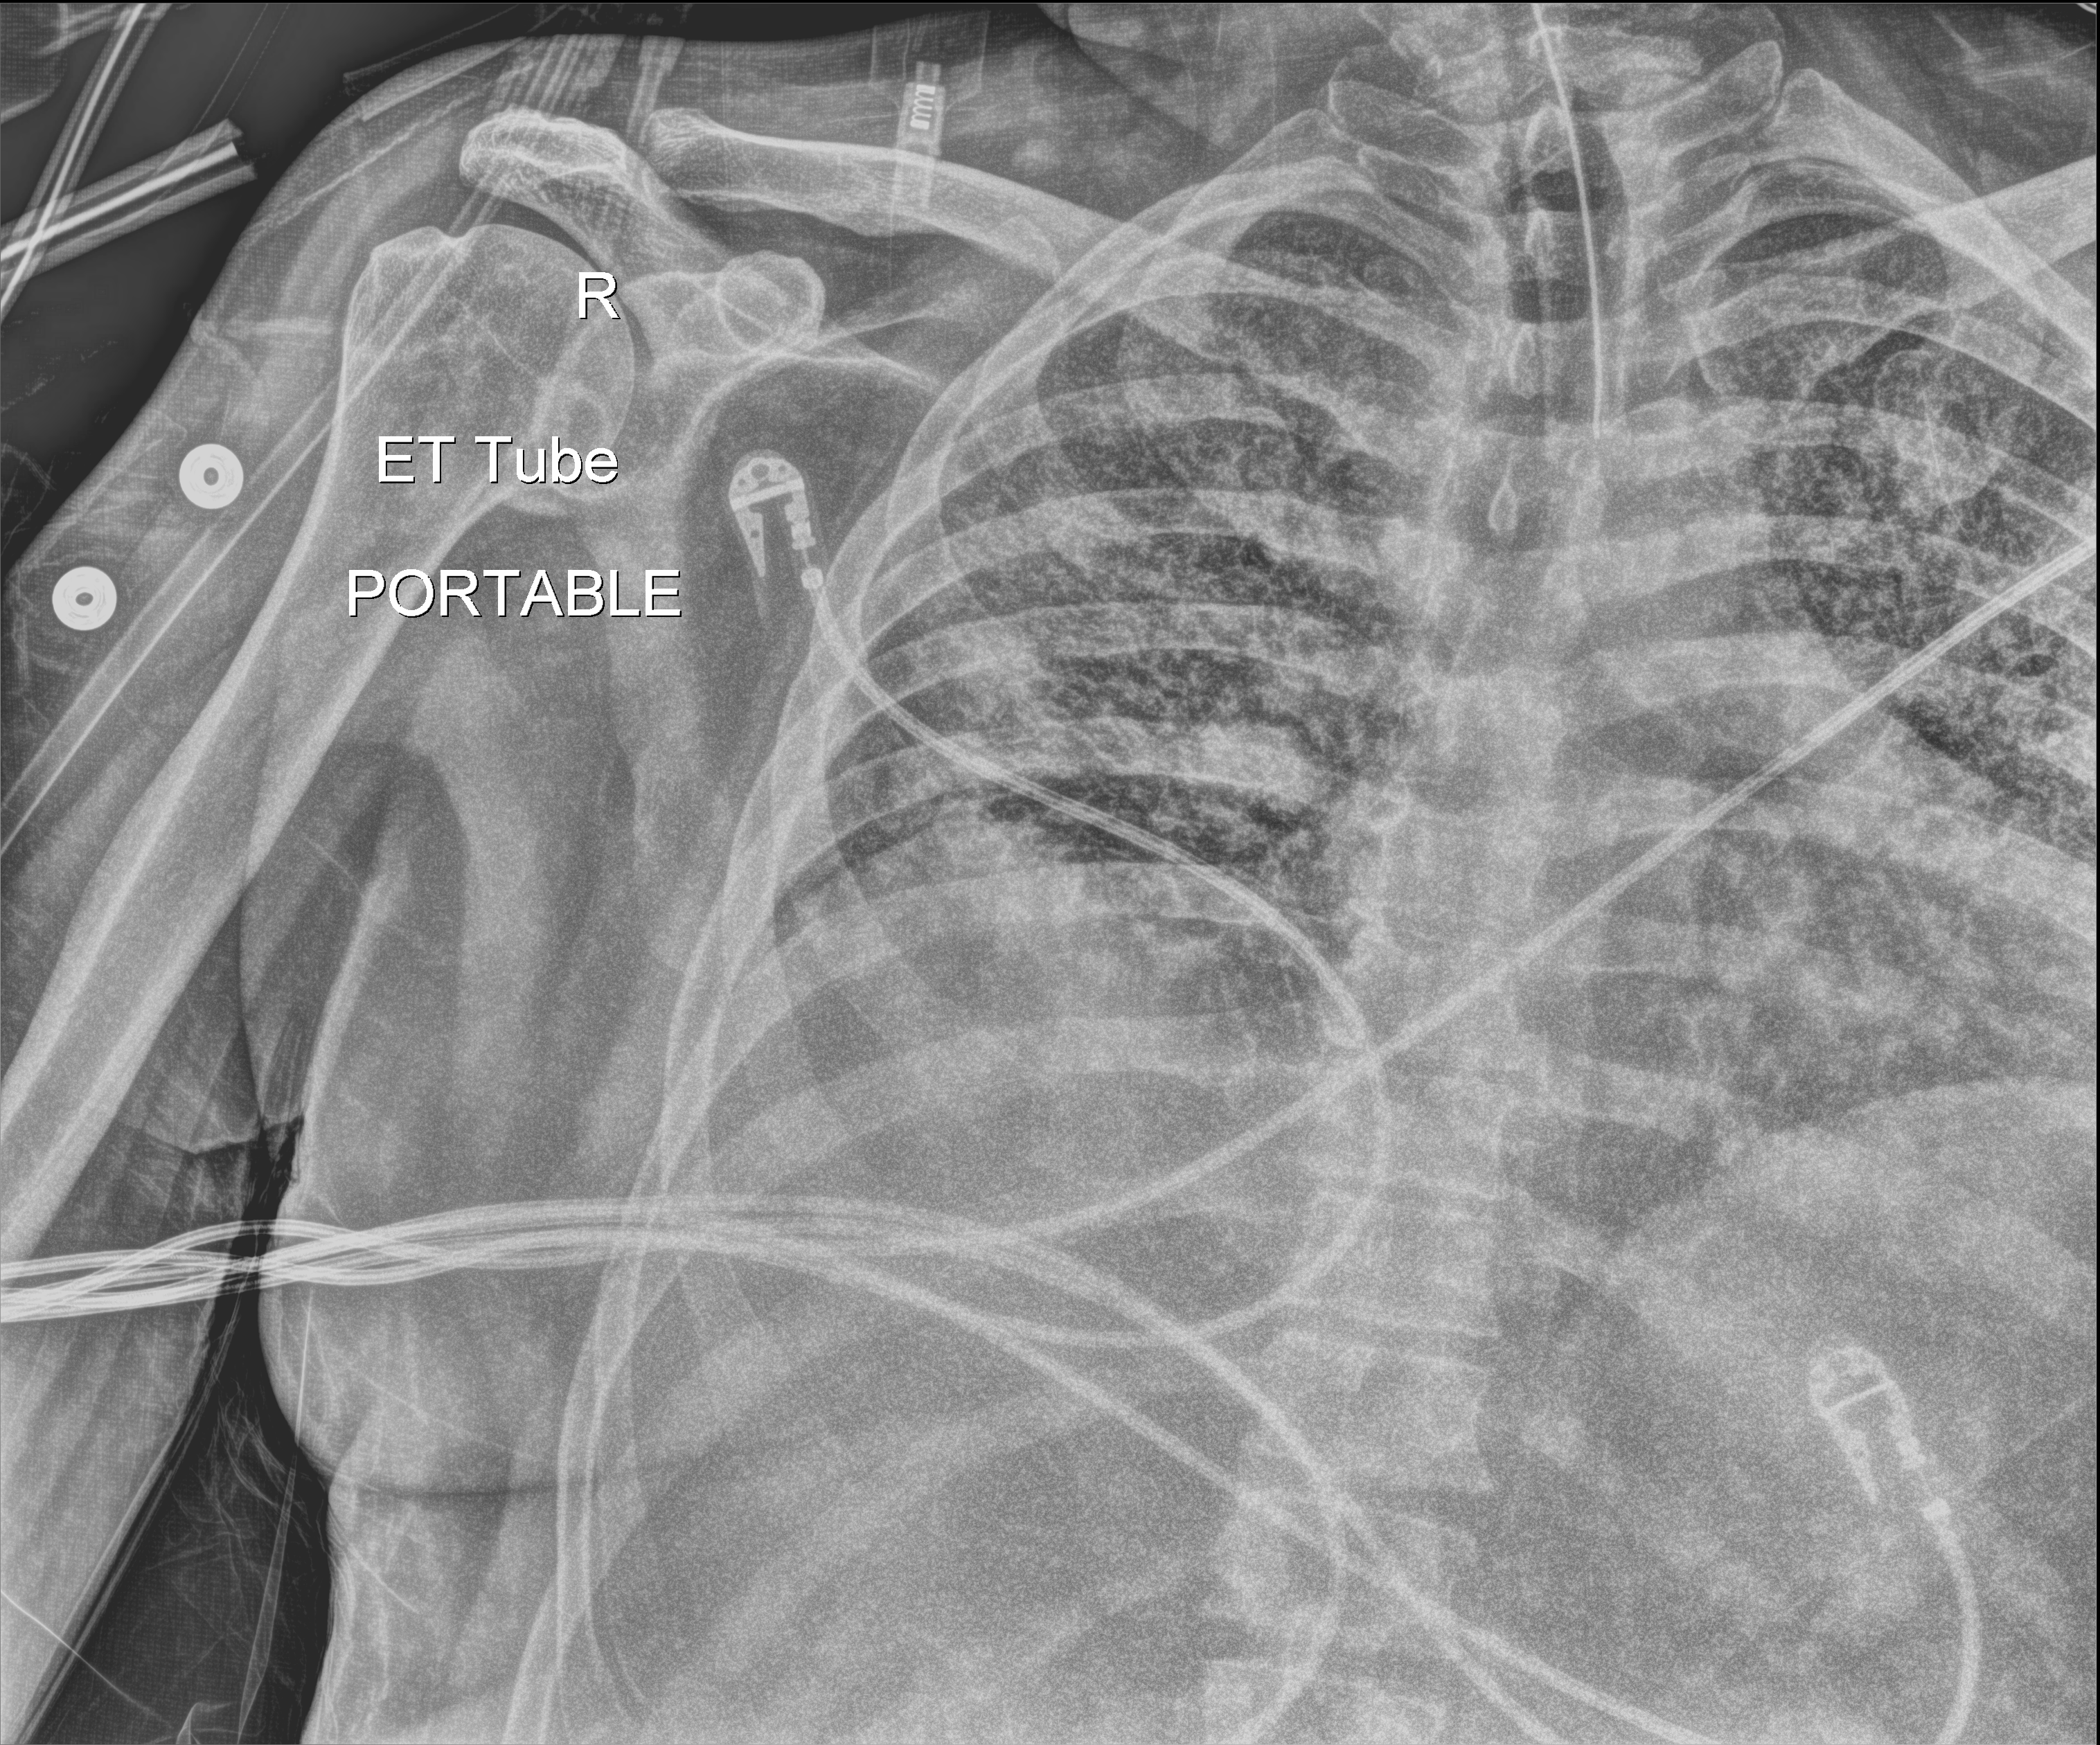
Chest radiograph, anteroposterior (AP) projection. Male patient hospitalised with COVID-19, age 18–59 years.
Hospital-stay facts (about this admission, not read from this image; timing relative to this image not recorded): diabetes (admission record): no; mechanically ventilated during this hospital stay: yes; length of hospital stay: 80 days.